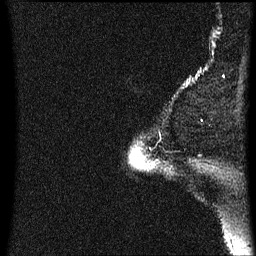
Breast MRI (dynamic contrast-enhanced), one sagittal slice. Slice 58 of 60 in the series (ordered by position). Dynamic contrast-enhanced series, image 2 of 3 at this slice position (ordered by acquisition). 1.5 T. TE 4.2 ms, TR 8.4 ms. 256 × 256 image matrix. Female patient, age 54 years. Case-level facts recorded for this patient, not image findings: setting: breast cancer imaged before/during neoadjuvant chemotherapy; receptor status: HR-positive, HER2-negative.
Annotated regions visible in this slice (semi-automatic segmentation, software-assisted and operator-edited):
- analysis volume of interest (the breast-tissue region the enhancement analysis was run in; not a lesion): box from (x=134, y=148) to (x=150, y=169) px
- tumour enhancement mask (voxels above the 70 % enhancement threshold inside the analysis volume of interest): (x=136, y=162)–(x=141, y=167)